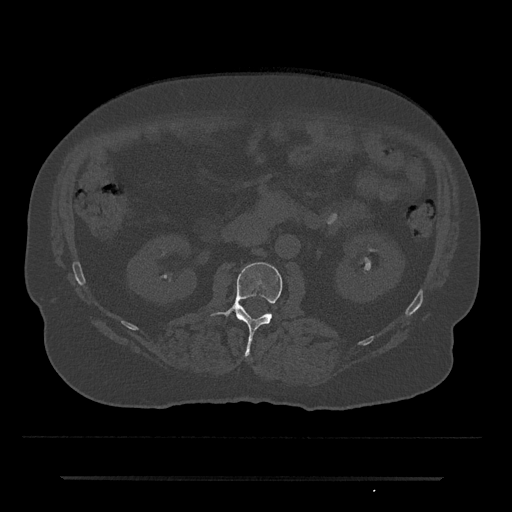
CT including the spine, one axial slice; slice 7 of 797 in the series (ordered by position); reconstruction kernel Br40s/3; 120 kVp; bone window (W 1800 / L 400 HU); 0.5 mm slice thickness; 512 × 512 image matrix, field of view 437 × 437 mm. Male patient, age 69 years. From the clinical record (not read from this slice): primary cancer: prostate.
Outlined on this slice (semi-automatic segmentation, software-assisted and operator-edited):
- L2 vertebra: bounding box <210,262,282,356> (left, top, right, bottom; pixels)